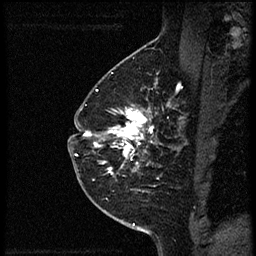
Breast MRI (dynamic contrast-enhanced), one sagittal slice; position 39 of 56 along the scan axis; dynamic contrast-enhanced study with each time point stored as its own series, time point 2 of 4 at this slice position (early post-contrast, ordered by acquisition time); 1.5 T; TE 4.2 ms, TR 18.9 ms; 256 × 256 image matrix, field of view 200 × 200 mm. Female patient. From the clinical record (not read from this slice): setting: breast cancer imaged before/during neoadjuvant chemotherapy; receptor status: HER2-positive.
Structures marked on this image (semi-automatic segmentation, software-assisted and operator-edited):
- analysis volume of interest (the breast-tissue region the enhancement analysis was run in; not a lesion): bounding box [x1, y1, x2, y2] px = [78, 89, 174, 189]
- tumour enhancement mask (voxels above the 100 % enhancement threshold inside the analysis volume of interest): [83, 105, 155, 174]